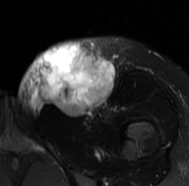
MRI of an extremity soft-tissue mass, one axial slice. Position 34 of 77 along the scan axis. T2-weighted fat-saturated. MR volume resampled by the dataset authors to the PET/CT grid (not the native acquisition matrix). 189 × 186 image matrix. Female patient. Case-level facts recorded for this patient, not image findings: histological type: leiomyosarcoma; grade: high; site of the primary tumour: groin.
Outlined on this slice (expert contour drawn on MRI and transferred to this co-registered scan by the dataset authors):
- gross tumour volume including surrounding oedema: bounding box (x1, y1, x2, y2) in pixels: (17, 36, 116, 119)
- gross tumour volume (mass): (38, 43, 114, 115)